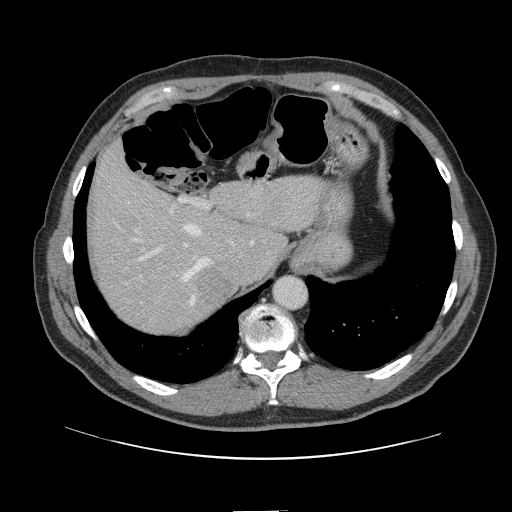
Contrast-enhanced abdominal CT, one axial slice. Slice 110 of 161 in the series (ordered by position). 120 kVp. Intravenous contrast given. Soft-tissue window (W 400 / L 40 HU). 2.5 mm slice thickness. 512 × 512 image matrix, field of view 412 × 412 mm. Male patient, age 66 years. From the clinical record (not read from this slice): diagnosis: colorectal cancer liver metastases, imaged before liver resection; multiple liver metastases: no; largest metastasis: 3.5 cm; disease in both lobes: no.
Annotated regions visible in this slice (outlined manually by an expert reader):
- hepatic veins: bounding box <133,213,250,306> (left, top, right, bottom; pixels)
- liver: <92,147,320,333>
- planned liver remnant (the part of the liver to remain after resection): <92,147,320,306>
- portal vein (with intrahepatic branches): <135,198,211,279>
- liver metastasis: <197,266,234,306>